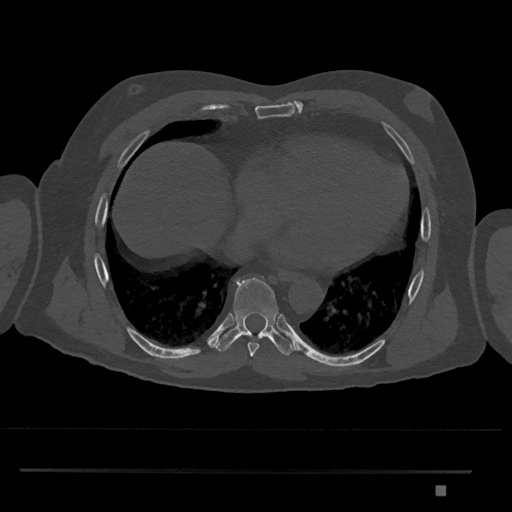
CT including the spine, one axial slice; slice 1128 of 1134 in the series (ordered by position); bone window (W 1800 / L 400 HU); 0.5 mm slice thickness; 512 × 512 image matrix, field of view 429 × 429 mm. Male patient, age 65 years. From the clinical record (not read from this slice): primary cancer: prostate.
Outlined on this slice (semi-automatic segmentation, software-assisted and operator-edited):
- T8 vertebra: bounding box [x1, y1, x2, y2] px = [215, 277, 296, 356]